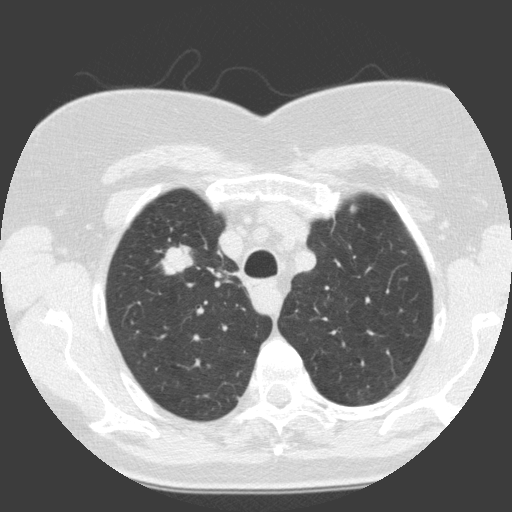
Low-dose screening chest CT, one axial slice. Slice 117 of 146 in the series (ordered by position). 120 kVp. Lung window (W 1500 / L -600 HU). 2 mm slice thickness. 512 × 512 image matrix, field of view 300 × 300 mm.
Annotated regions visible in this slice (manually delineated by an expert):
- lesion 1 (tumor, upper lobe of right lung): box from (x=157, y=244) to (x=194, y=275) px